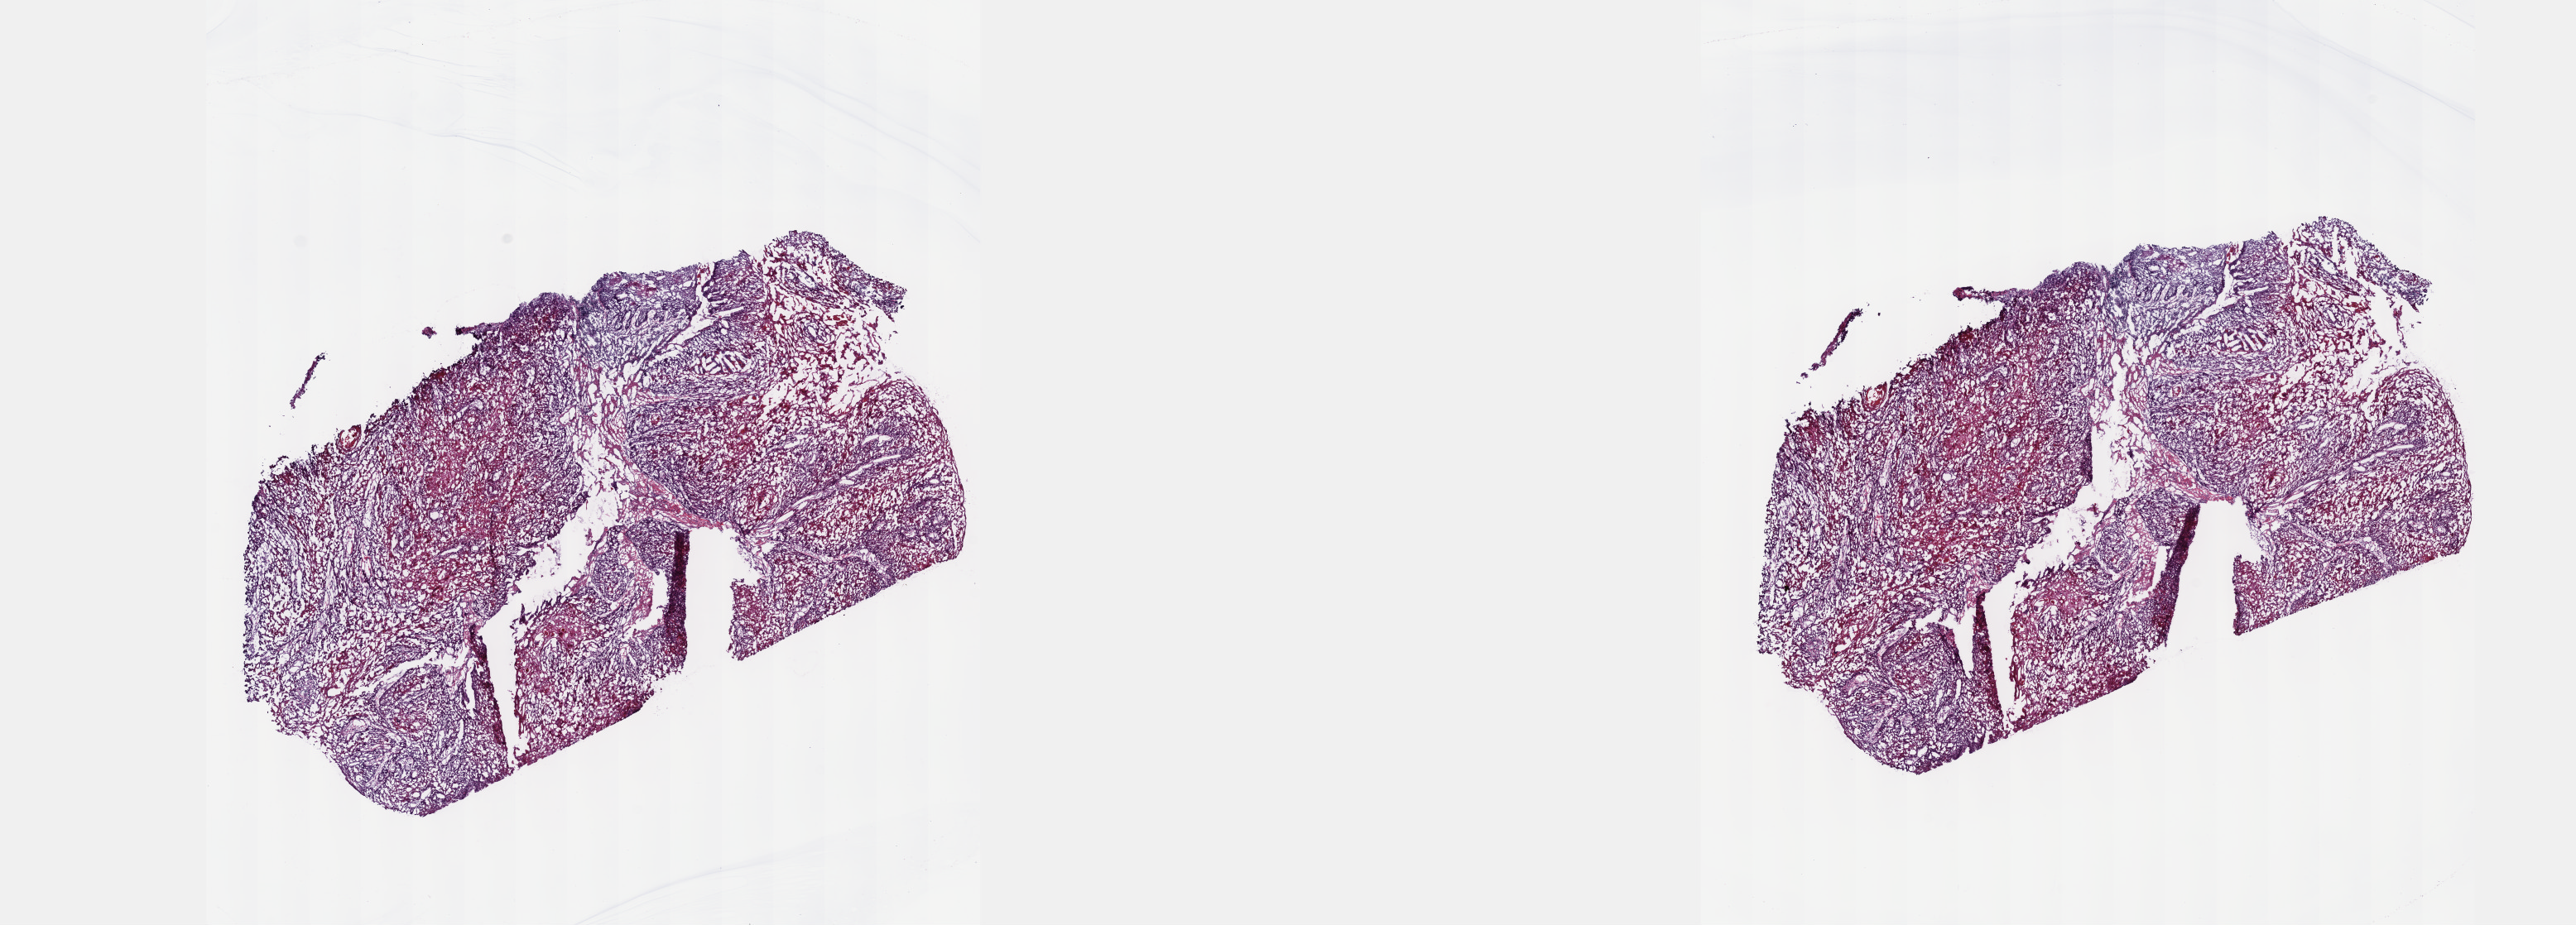
Whole-slide histology image, Hematoxylin and eosin (H&E) stained, whole scanned area (about 25.1 x 9.0 mm) shown as a low-resolution overview, frozen section, sample: primary tumour, esophagus. Patient: female, age at initial diagnosis 63 years. Histologic grade: G2 (moderately differentiated). Composition of this section per pathologist review: tumour cells 60%, tumour nuclei 60%, normal cells 0%, stromal cells 30%, necrosis 10%. Inflammatory infiltration, as recorded: lymphocyte infiltration 40%, monocyte infiltration 20%, neutrophil infiltration 20%.
TNM: T2 N0 M0. AJCC pathologic stage: IIA (7th edition). Lymph nodes positive (case pathology): 0 of 9 examined. Pathologic diagnosis: Squamous cell carcinoma, NOS (middle third of esophagus).